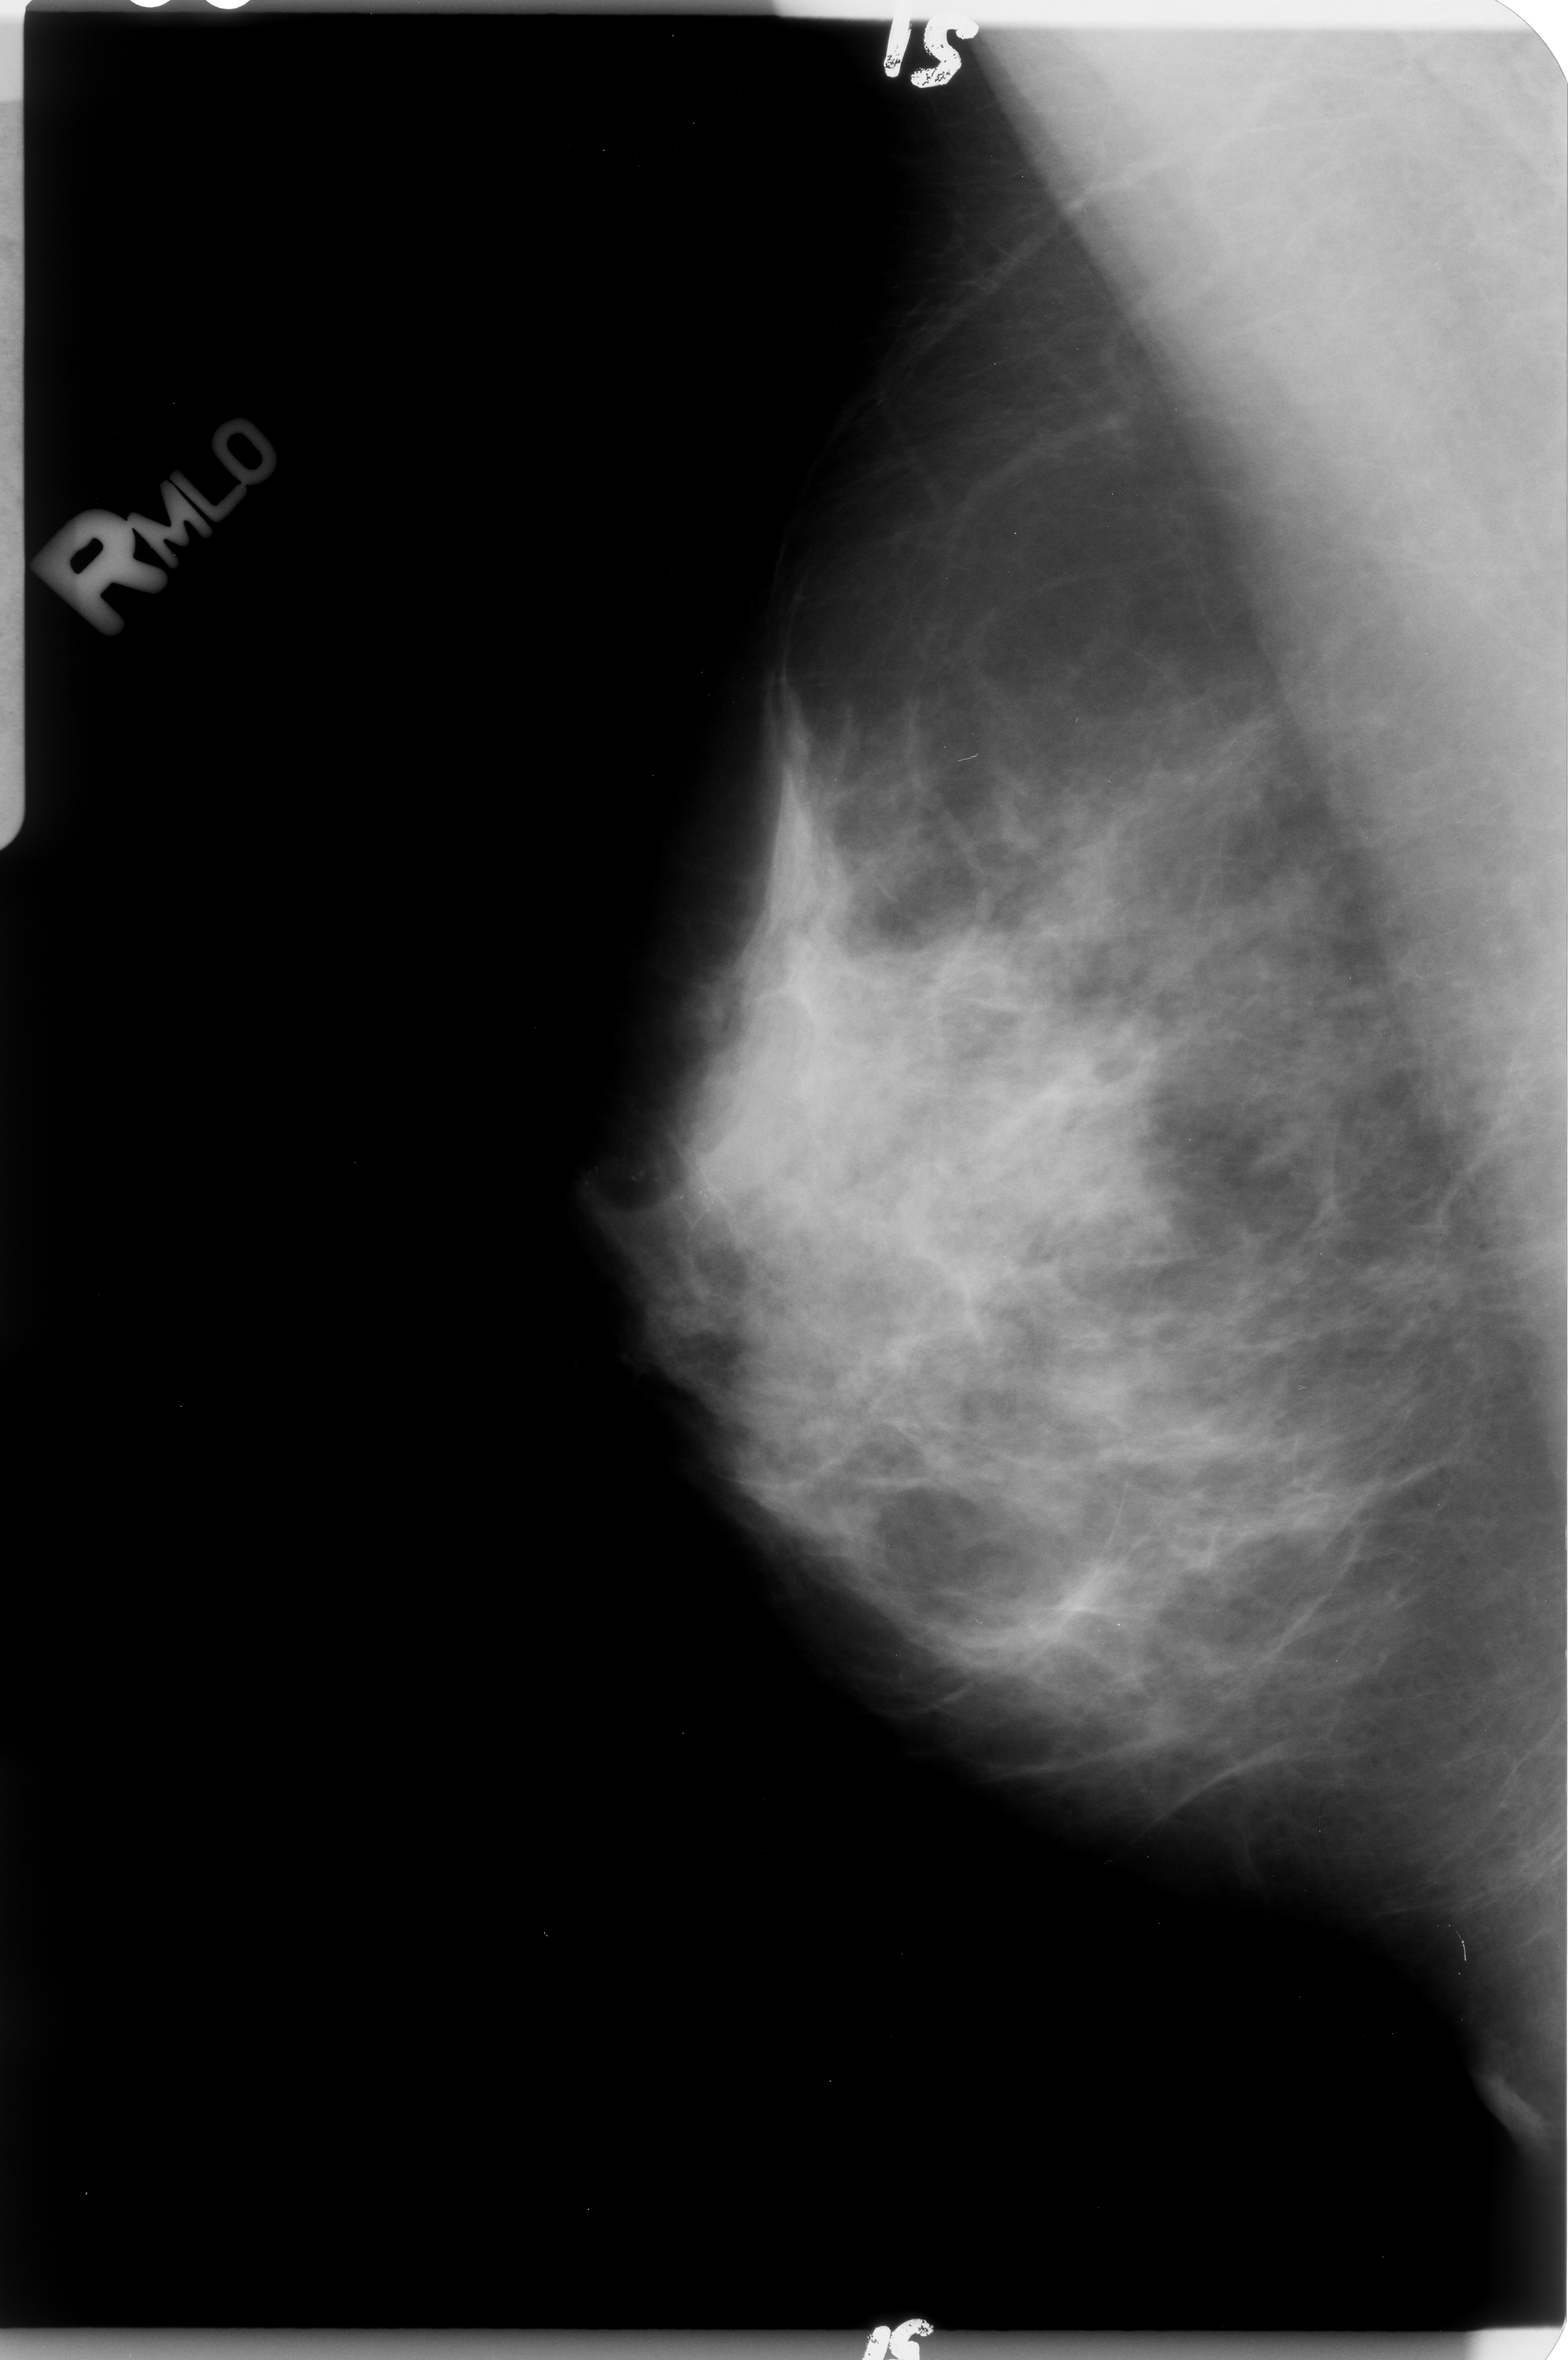
Mammogram (digitized film). Right breast. Mediolateral oblique (MLO) view. BI-RADS breast density category 3 (scale 1–4). 1568 × 2360 image matrix.
Expert-marked regions of interest on this image (one box per marked abnormality):
- calcifications, morphology pleomorphic, distribution linear; BI-RADS assessment category 4; pathology result (as recorded, not read from the image): malignant: box from (x=652, y=1176) to (x=813, y=1273) px